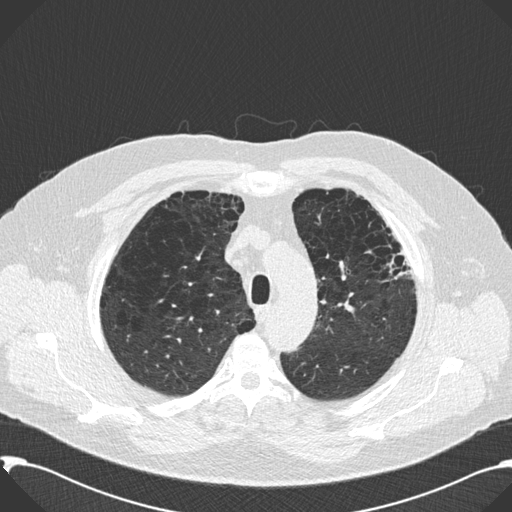
Axial slice from a low-dose chest CT screening exam; second screening round (one year after baseline); lung window (W 1500 / L -600 HU); 2 mm slice thickness; slice 40 of 199 in the series. Male, age 59 years at enrolment. Current smoker at enrolment.
Lesion marked by an expert reader, box from (x=364, y=225) to (x=416, y=300) px. Screening reader's record for this exam: no non-calcified nodule ≥4 mm recorded. Official screen result: negative screen, significant abnormalities not suspicious for lung cancer.